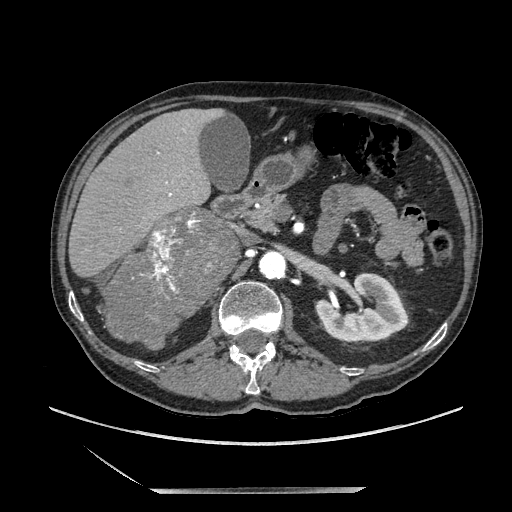
Contrast-enhanced abdominal CT, one axial slice. Slice 109 of 243 in the series (ordered by position). Soft-tissue window (W 400 / L 40 HU). 512 × 512 image matrix, field of view 420 × 420 mm. Male patient. Case-level facts recorded for this patient, not image findings: diagnosis: adrenocortical carcinoma; tumour side: right adrenal; tumour size at pathology: 16 cm; Ki-67 index: 17 %; stage (as recorded): 3.
Structures marked on this image (semi-automatic segmentation, software-assisted and operator-edited):
- mass: box from (x=109, y=213) to (x=231, y=341) px